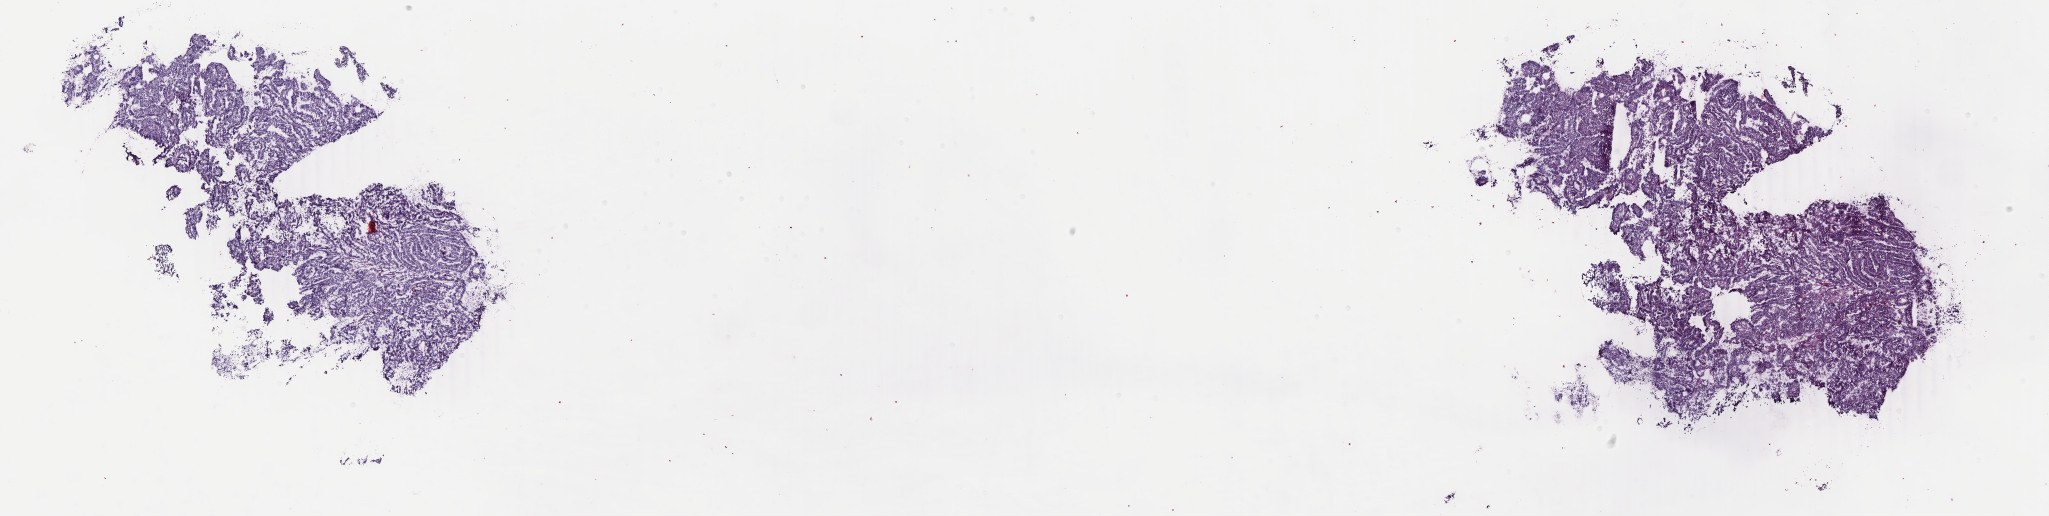
H&E-stained whole-slide image, a low-resolution overview of the entire scanned area, about 32.6 x 8.2 mm (slide scanned at 40x); frozen section from the bottom of the tissue portion; primary tumour sample from the uterus. Patient sex: female. Histologic grade: G3 (poorly differentiated). Composition of this section per pathologist review: tumour cells 100%, tumour nuclei 90%, normal cells 0%, stromal cells 0%, necrosis 0%. Infiltration values recorded for this section: lymphocyte infiltration 0%, monocyte infiltration 0%, neutrophil infiltration 0%.
FIGO stage: IVB. Pathologic diagnosis: Serous cystadenocarcinoma, NOS.